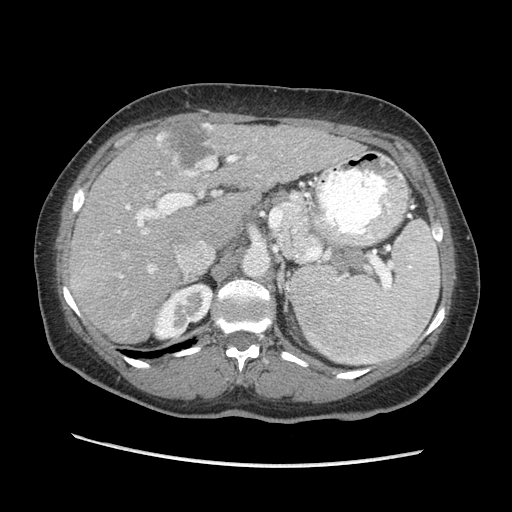
Contrast-enhanced abdominal CT (liver protocol), one axial slice; position 133 of 170 along the scan axis; reconstruction kernel STANDARD; 140 kVp; soft-tissue window (W 400 / L 40 HU); 2.5 mm slice thickness; 512 × 512 image matrix, field of view 360 × 360 mm. From the clinical record (not read from this slice): diagnosis: hepatocellular carcinoma (patient treated with transarterial chemoembolisation; whether this scan precedes or follows treatment is not stated here); TNM stage (as recorded): Stage-II; Child-Pugh class: A.
Outlined on this slice (semi-automatically segmented with operator editing):
- liver parenchyma outside the tumour (the mass and vessels are separate outlines, so this box may not span the whole liver): bounding box <68,122,364,342> (left, top, right, bottom; pixels)
- mass: <156,122,212,168>
- liver vessels: <117,123,297,315>